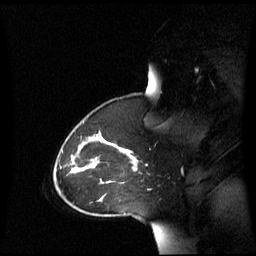
Breast MRI (dynamic contrast-enhanced), one sagittal slice. Slice 43 of 60 in the series (ordered by position). Dynamic contrast-enhanced series, image 2 of 3 at this slice position (ordered by acquisition). 1.5 T. TE 4.2 ms, TR 8.4 ms. 256 × 256 image matrix, field of view 270 × 270 mm. Female patient, age 43 years. Case-level facts recorded for this patient, not image findings: setting: breast cancer imaged before/during neoadjuvant chemotherapy; receptor status: triple-negative.
Outlined on this slice (semi-automatic segmentation, software-assisted and operator-edited):
- analysis volume of interest (the breast-tissue region the enhancement analysis was run in; not a lesion): box from (x=69, y=137) to (x=138, y=198) px
- tumour enhancement mask (voxels above the 70 % enhancement threshold inside the analysis volume of interest): (x=119, y=147)–(x=138, y=165)